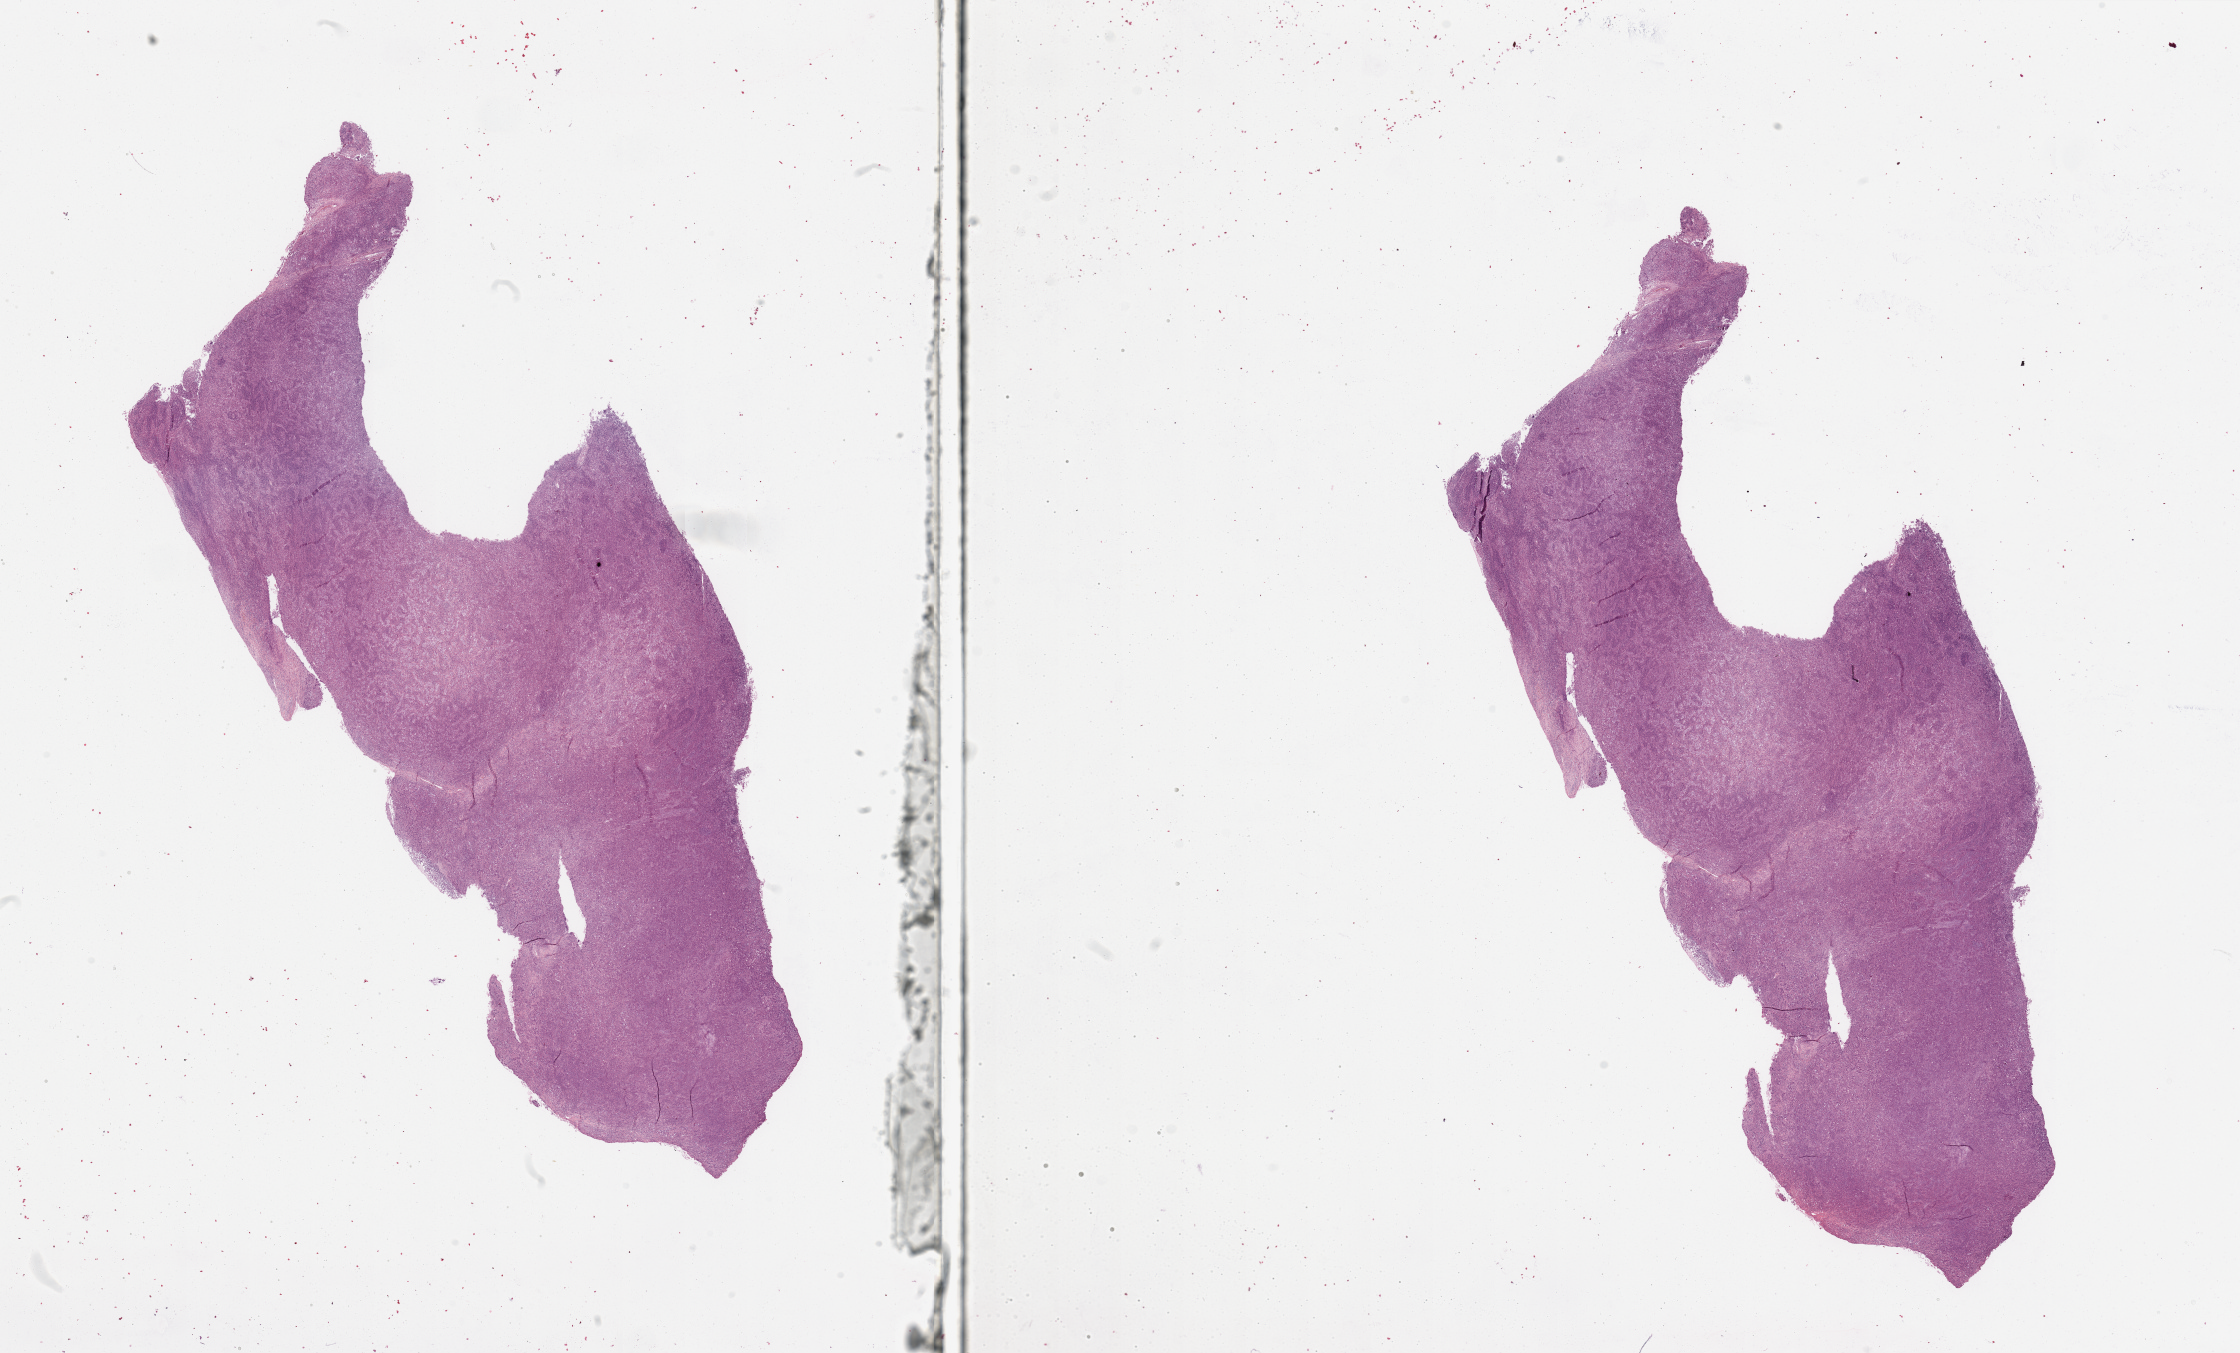
Digitized H&E tissue section (whole slide) — shown as a low-resolution overview of the whole scanned area (about 35.4 x 21.4 mm, acquisition: 20x scan); melanoma tumour tissue; sampled site not recorded. Patient: female, age 53 years.
AJCC pathologic stage: IIIB. Diagnosis: Malignant melanoma, NOS. Primary tumour site (as recorded): trunk.